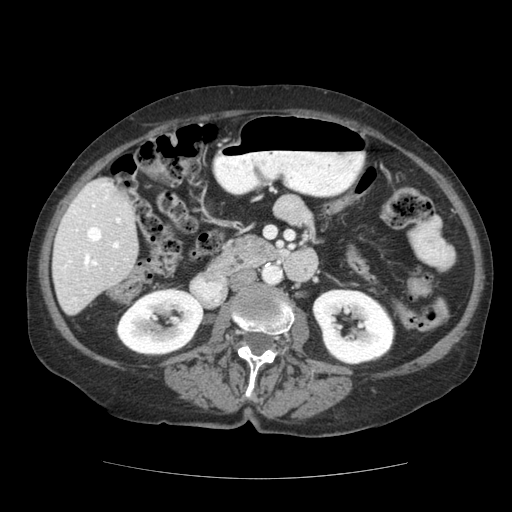
Contrast-enhanced abdominal CT (liver protocol), one axial slice. Position 52 of 111 along the scan axis. Soft-tissue window (W 400 / L 40 HU). 2.5 mm slice thickness. 512 × 512 image matrix. Case-level facts recorded for this patient, not image findings: diagnosis: hepatocellular carcinoma (patient treated with transarterial chemoembolisation; whether this scan precedes or follows treatment is not stated here); TNM stage (as recorded): Stage-I; Child-Pugh class: A; tumour differentiation: moderately-poorly differentiated; tumour nodularity: uninodular.
Outlined on this slice (semi-automatically segmented with operator editing):
- liver parenchyma outside the tumour (the mass and vessels are separate outlines, so this box may not span the whole liver): bounding box <52,178,138,314> (left, top, right, bottom; pixels)
- liver vessels: <60,183,121,300>